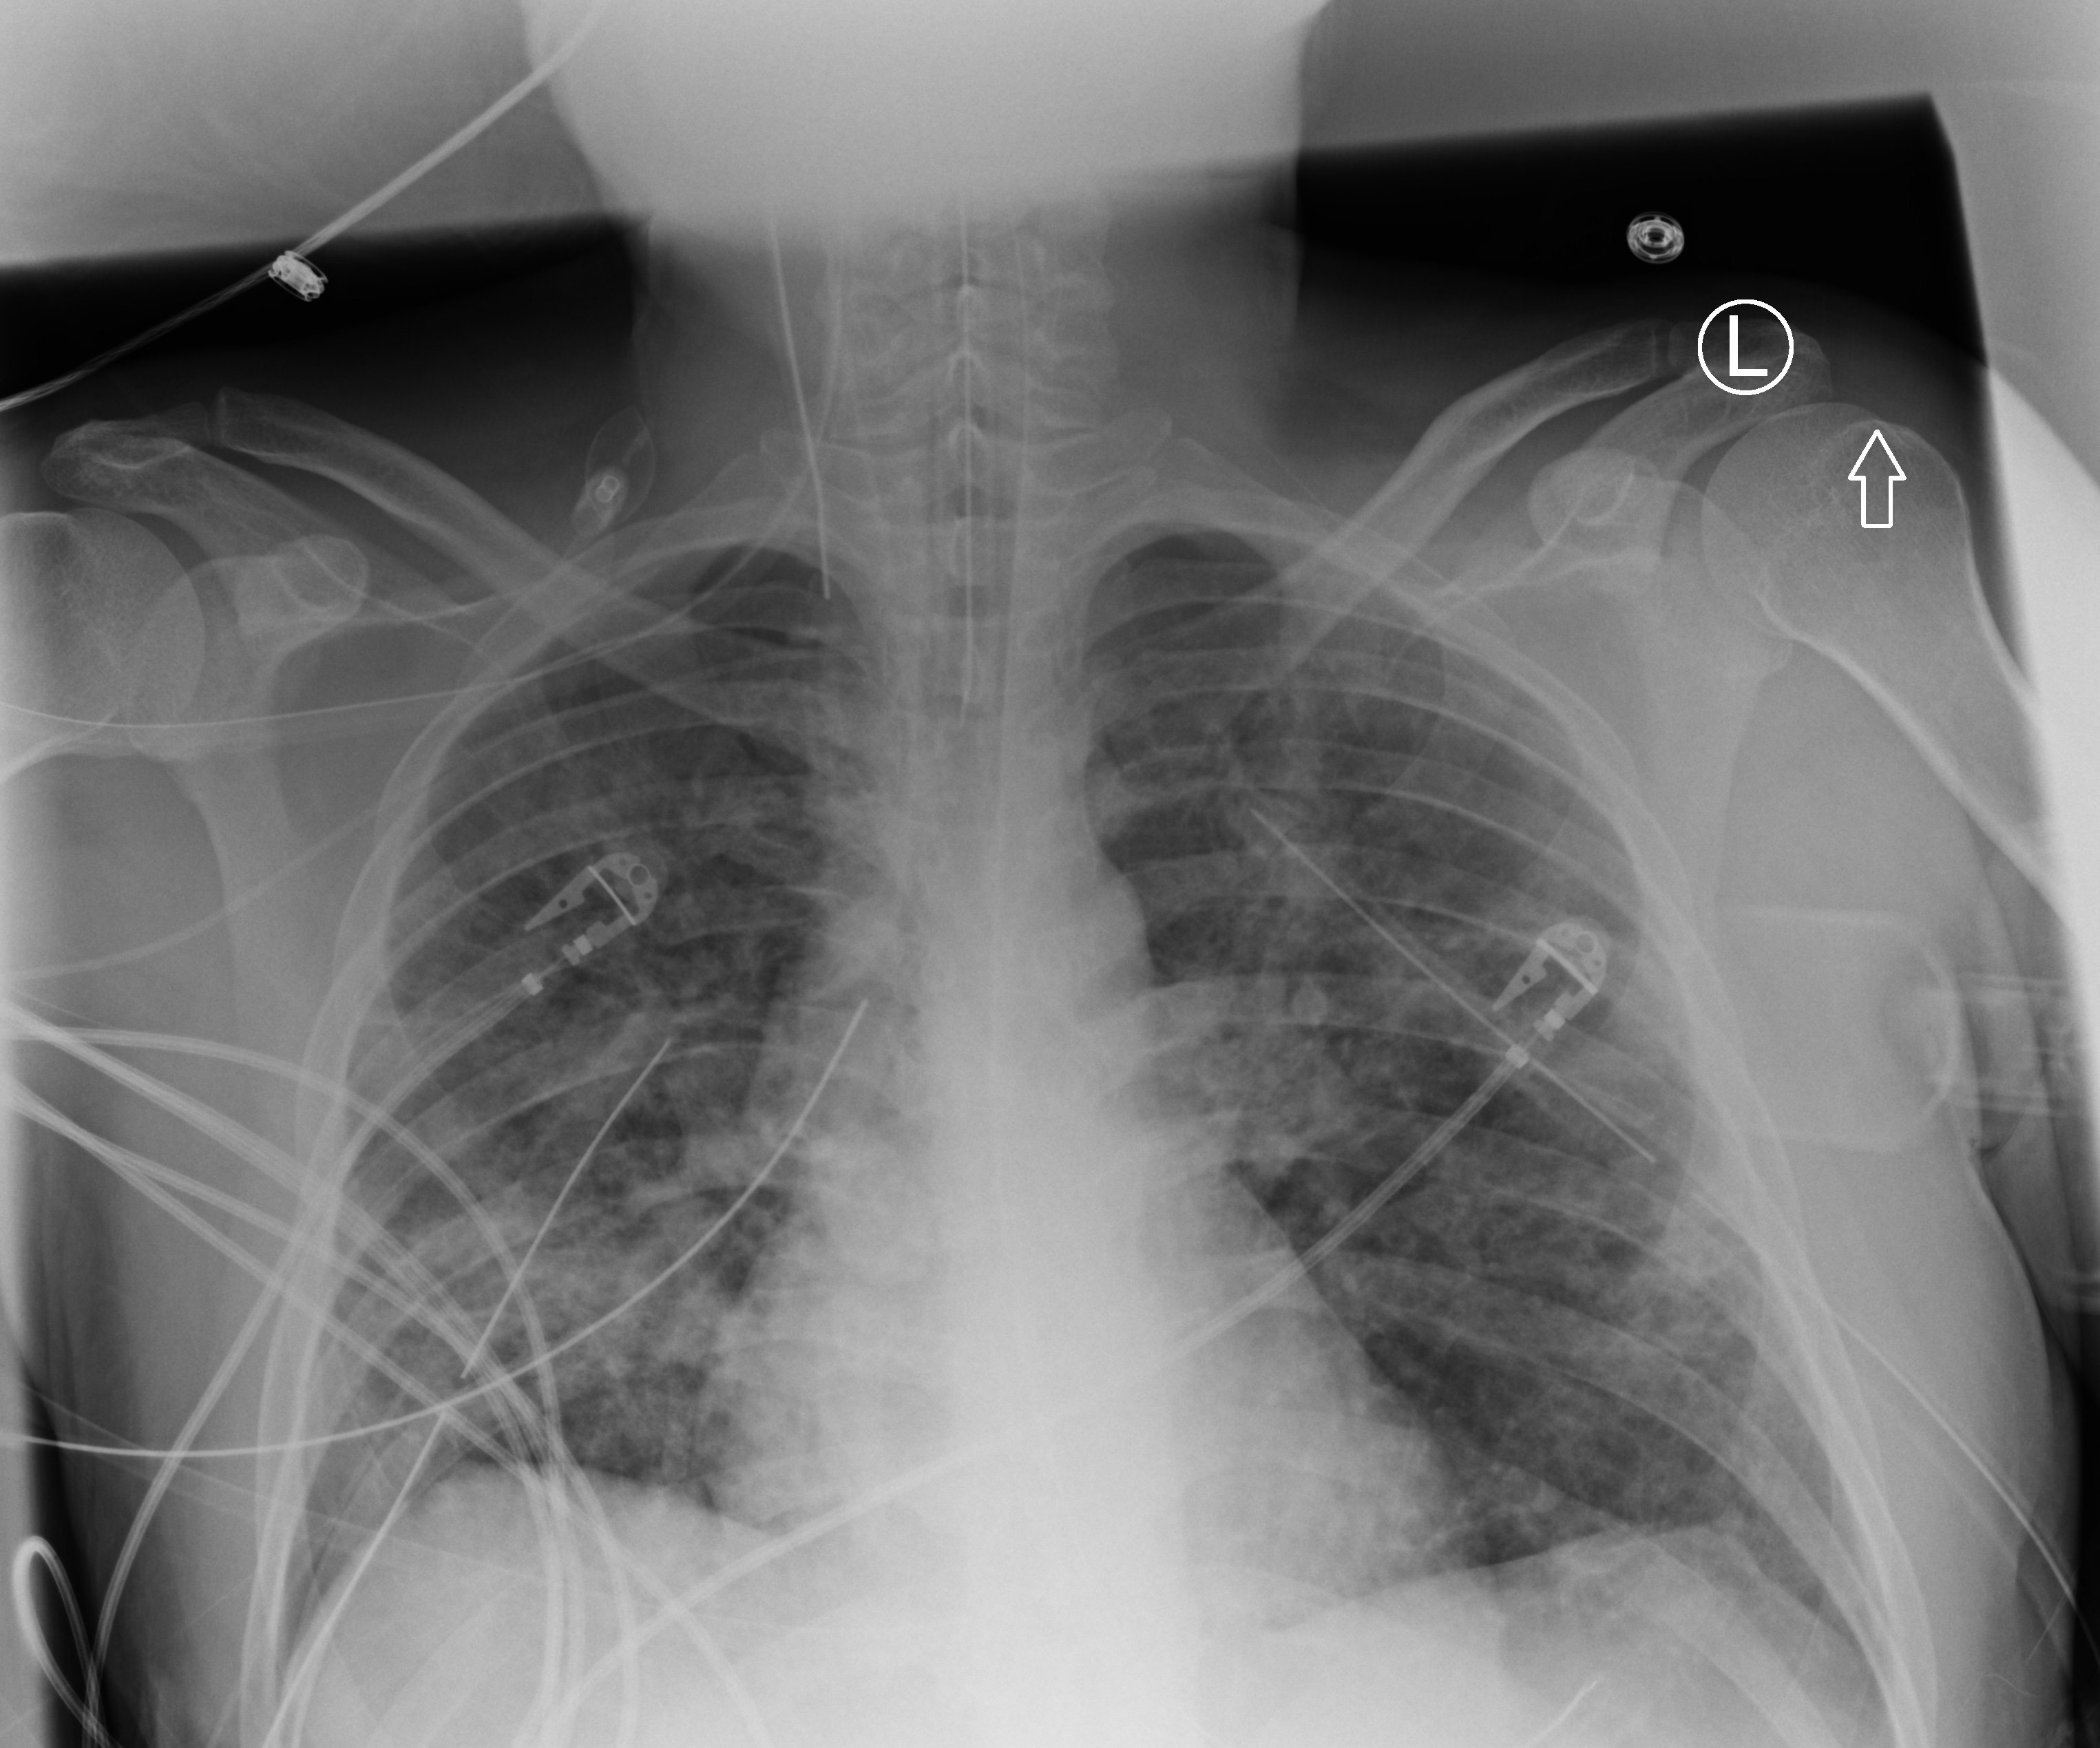
Portable chest radiograph; anteroposterior (AP) projection. Male patient hospitalised with COVID-19, age 18–59 years.
Admission-level facts for this patient (not findings on this image; timing relative to this image not recorded): length of hospital stay: 29 days.